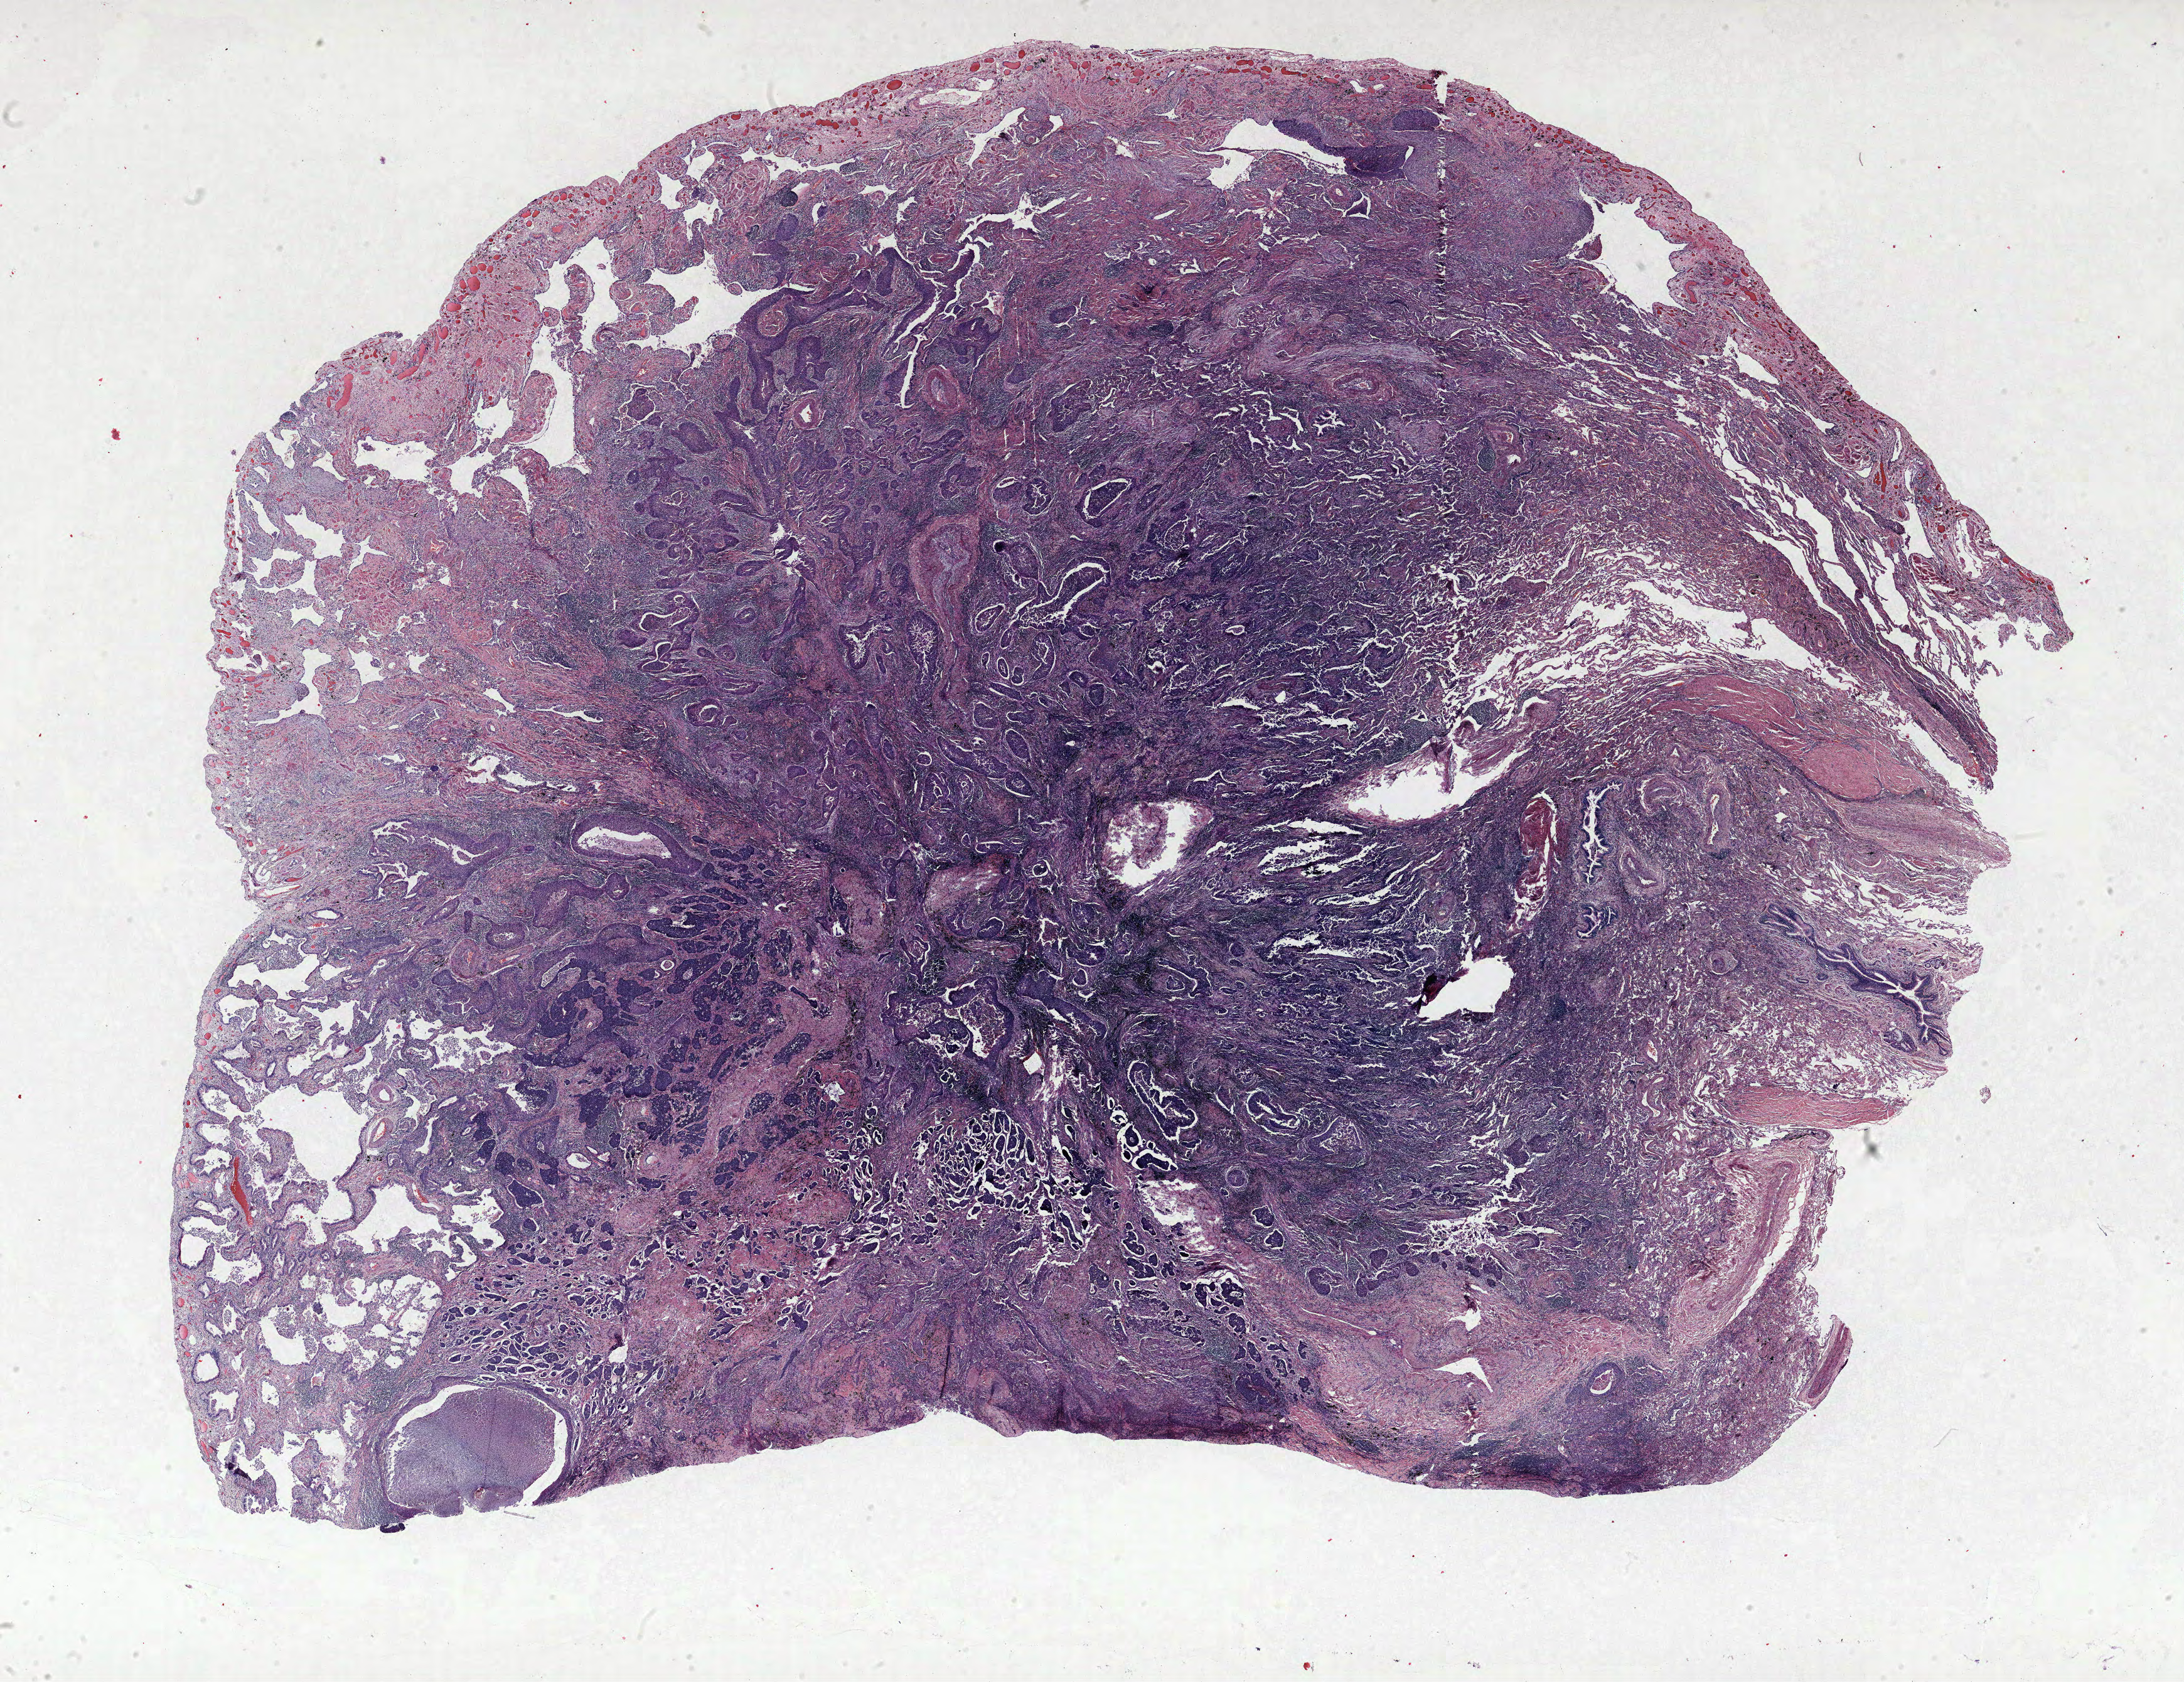
H&E whole-slide image — shown as a low-resolution overview of the whole scanned area (about 27.8 x 21.4 mm, slide scanned at 40x). Formalin-fixed paraffin-embedded (FFPE) section. Lung. Male, age 68 at enrolment. Grade: poorly differentiated (G3).
* tumour size (pathology): 30 mm
* participant's lung-cancer diagnosis: Adenosquamous carcinoma
* stage (AJCC 6th edition): IIIA
* primary tumour location (clinical record): right lower lobe